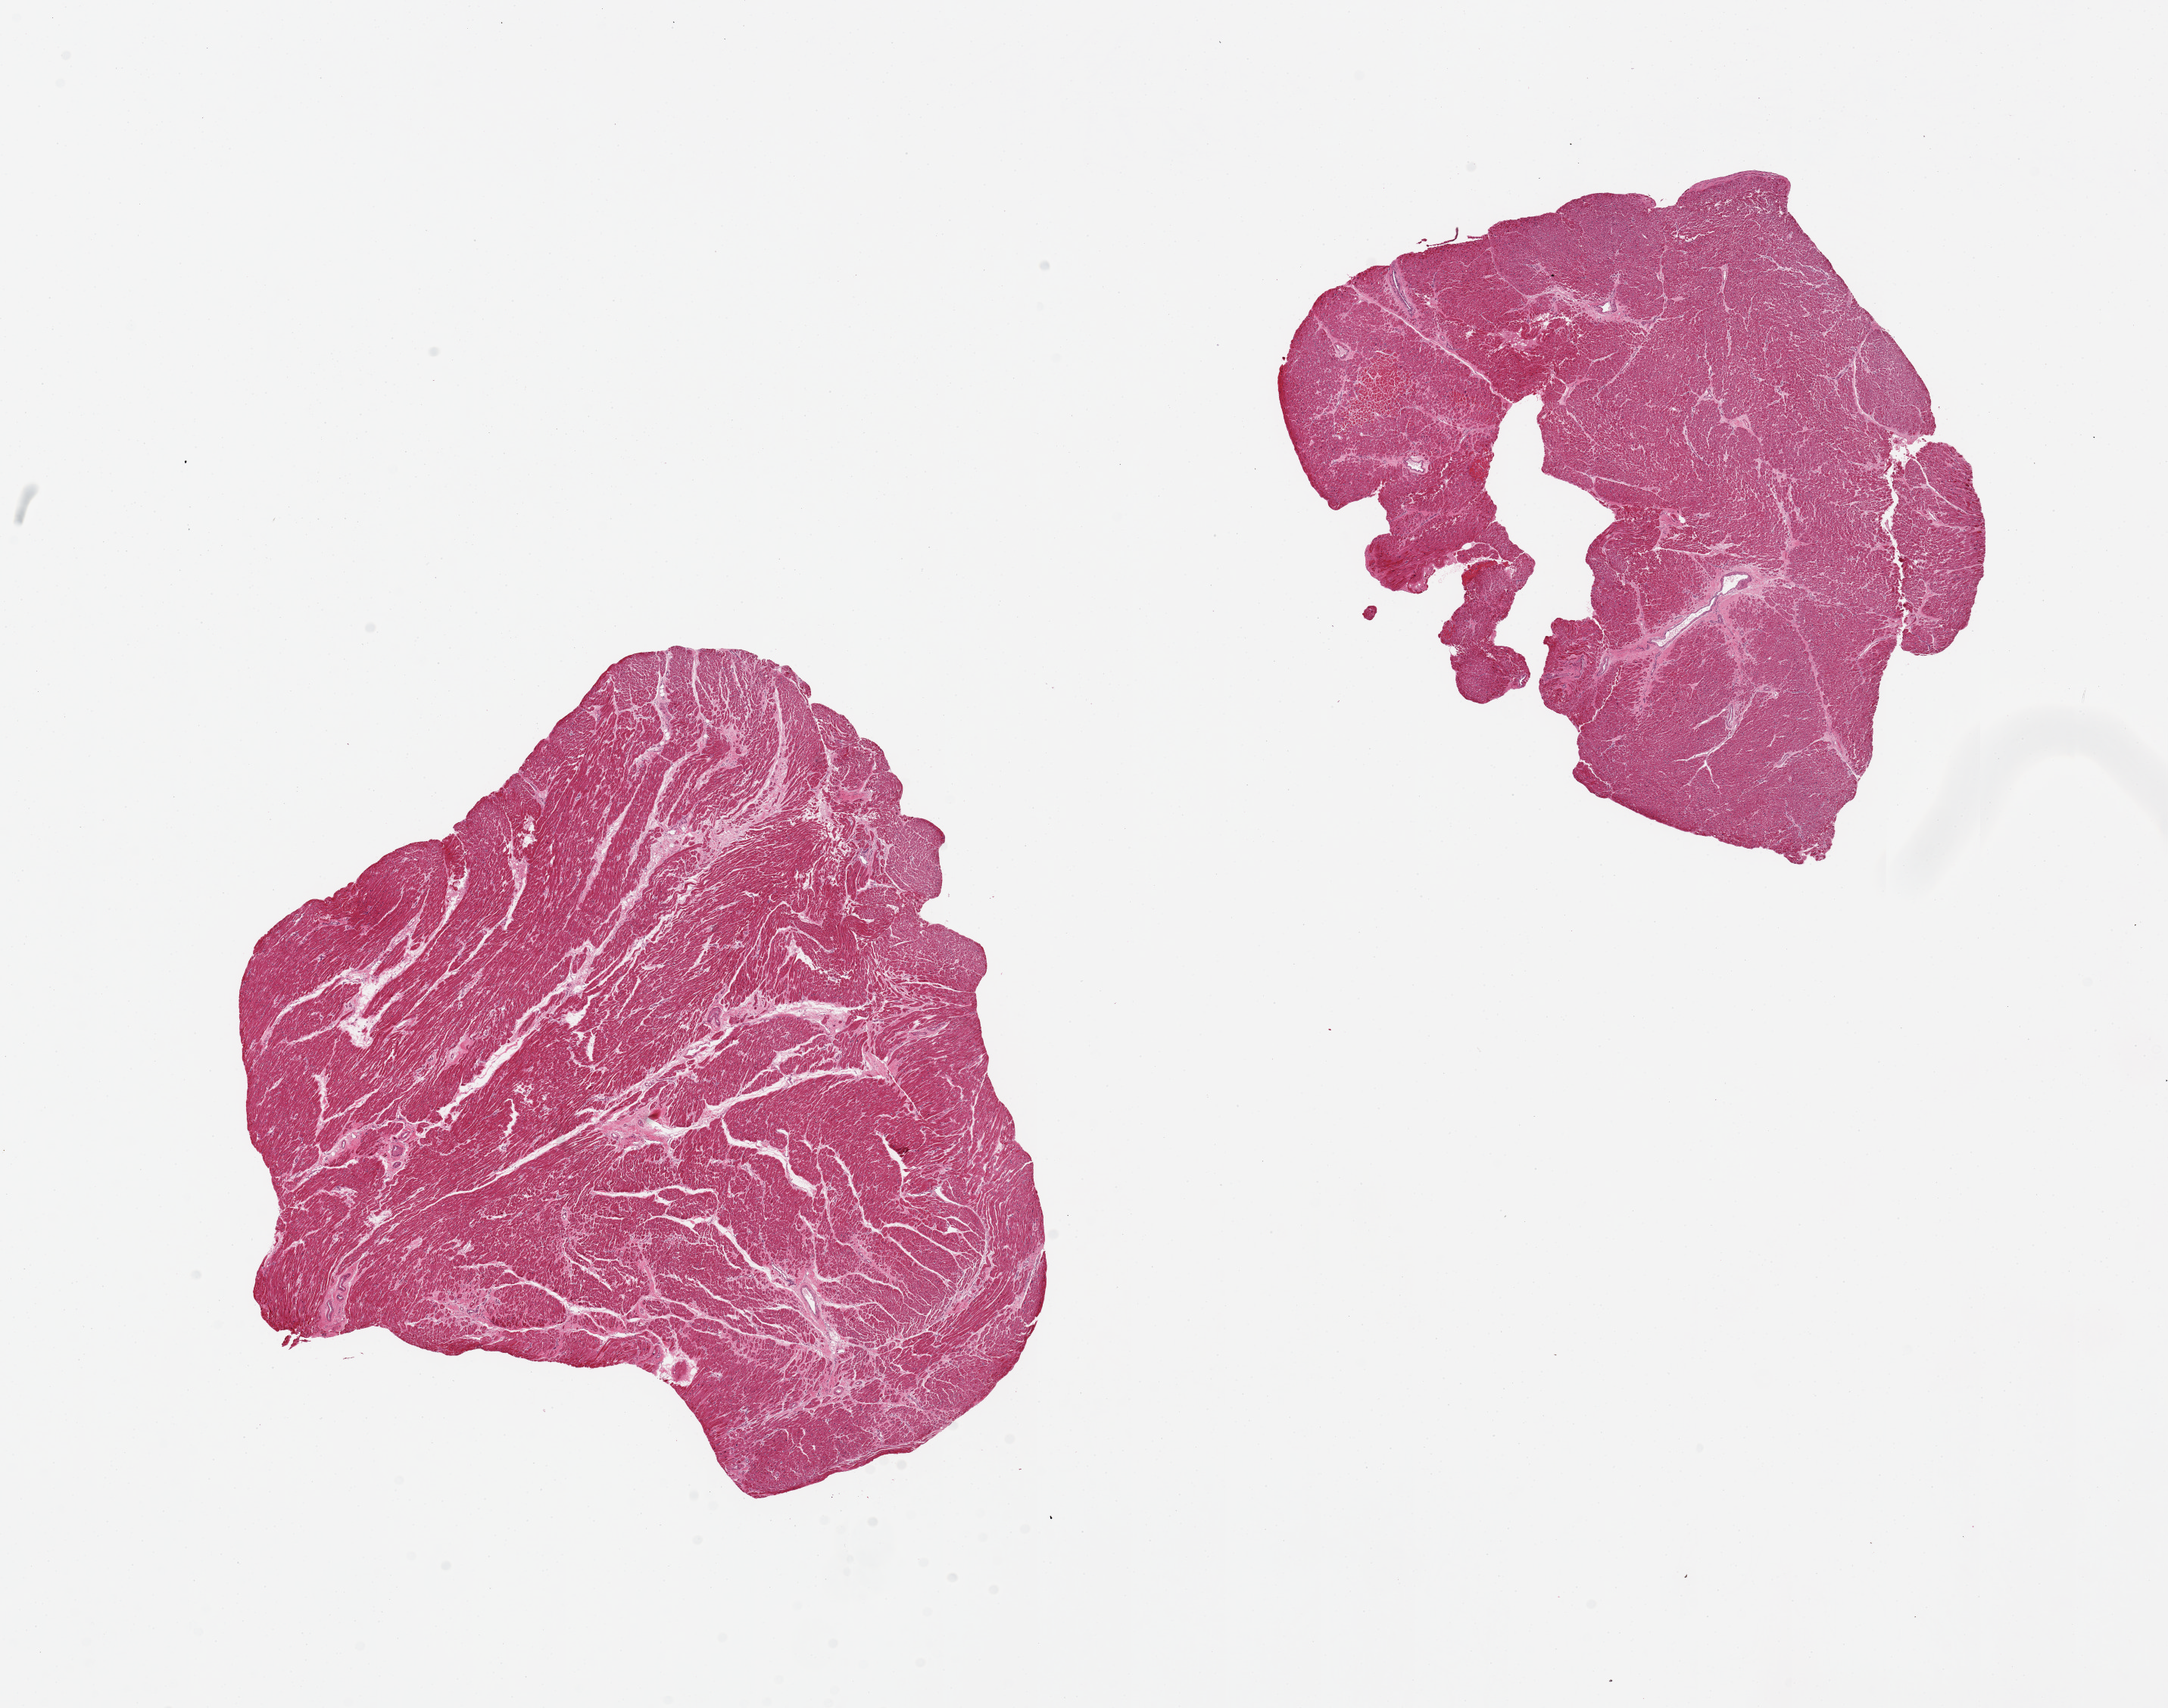
Digitized hematoxylin and eosin (H&E)-stained section, whole scanned area (about 22.6 x 17.8 mm) shown as a low-resolution overview; PAXgene-fixed paraffin-embedded (PFPE) section; target tissue: heart; donor tissue sample.
Review note (as recorded): 2 pieces, 9x9 & 8x6.5mm; patchy fibrosis, confluent, c/w remote infarct(s).